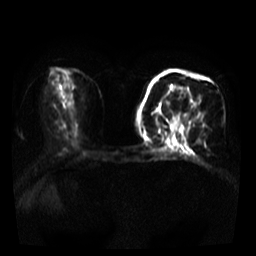
Breast MRI, one axial slice; slice 15 of 39 in the series (ordered by position); diffusion-weighted series; image 2 of 4 stored at this slice position (different b-values; order by instance number); 3 T; 256 × 256 image matrix, field of view 320 × 320 mm. Female patient.
Annotated regions visible in this slice (outlined manually by an expert reader):
- tumour on diffusion-weighted imaging: bounding box [x1, y1, x2, y2] px = [199, 113, 202, 117]